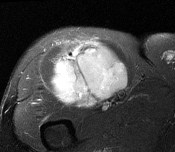
MRI of an extremity soft-tissue mass, one axial slice; slice 103 of 116 in the series (ordered by position); T2-weighted fat-saturated; MR volume resampled by the dataset authors to the PET/CT grid (not the native acquisition matrix); 3.27 mm slice thickness; 175 × 152 image matrix, field of view 171 × 148 mm. Male patient. Case-level facts recorded for this patient, not image findings: histological type: pleiomorphic leiomyosarcoma; grade: intermediate; site of the primary tumour: right thigh.
Outlined on this slice (expert contour drawn on MRI and transferred to this co-registered scan by the dataset authors):
- gross tumour volume including surrounding oedema: bounding box (x1, y1, x2, y2) in pixels: (51, 40, 128, 105)
- gross tumour volume (mass): (54, 40, 128, 105)